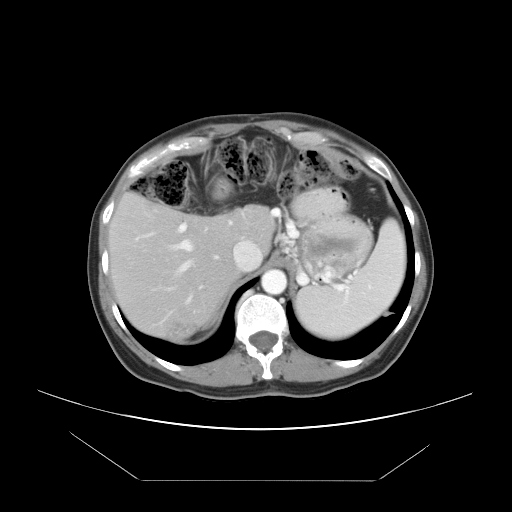
Contrast-enhanced abdominal CT, one axial slice; position 33 of 45 along the scan axis; 120 kVp; intravenous contrast given; soft-tissue window (W 400 / L 40 HU); 5 mm slice thickness; 512 × 512 image matrix. Female patient, age 52 years. Case-level facts recorded for this patient, not image findings: diagnosis: colorectal cancer liver metastases, imaged before liver resection; multiple liver metastases: yes; largest metastasis: 2.5 cm; chemotherapy before resection: yes.
Annotated regions visible in this slice (manually delineated by an expert):
- hepatic veins: bounding box <142,206,203,291> (left, top, right, bottom; pixels)
- liver: <111,196,273,339>
- planned liver remnant (the part of the liver to remain after resection): <111,196,273,318>
- portal vein (with intrahepatic branches): <143,221,233,258>
- liver metastasis: <169,325,195,336>